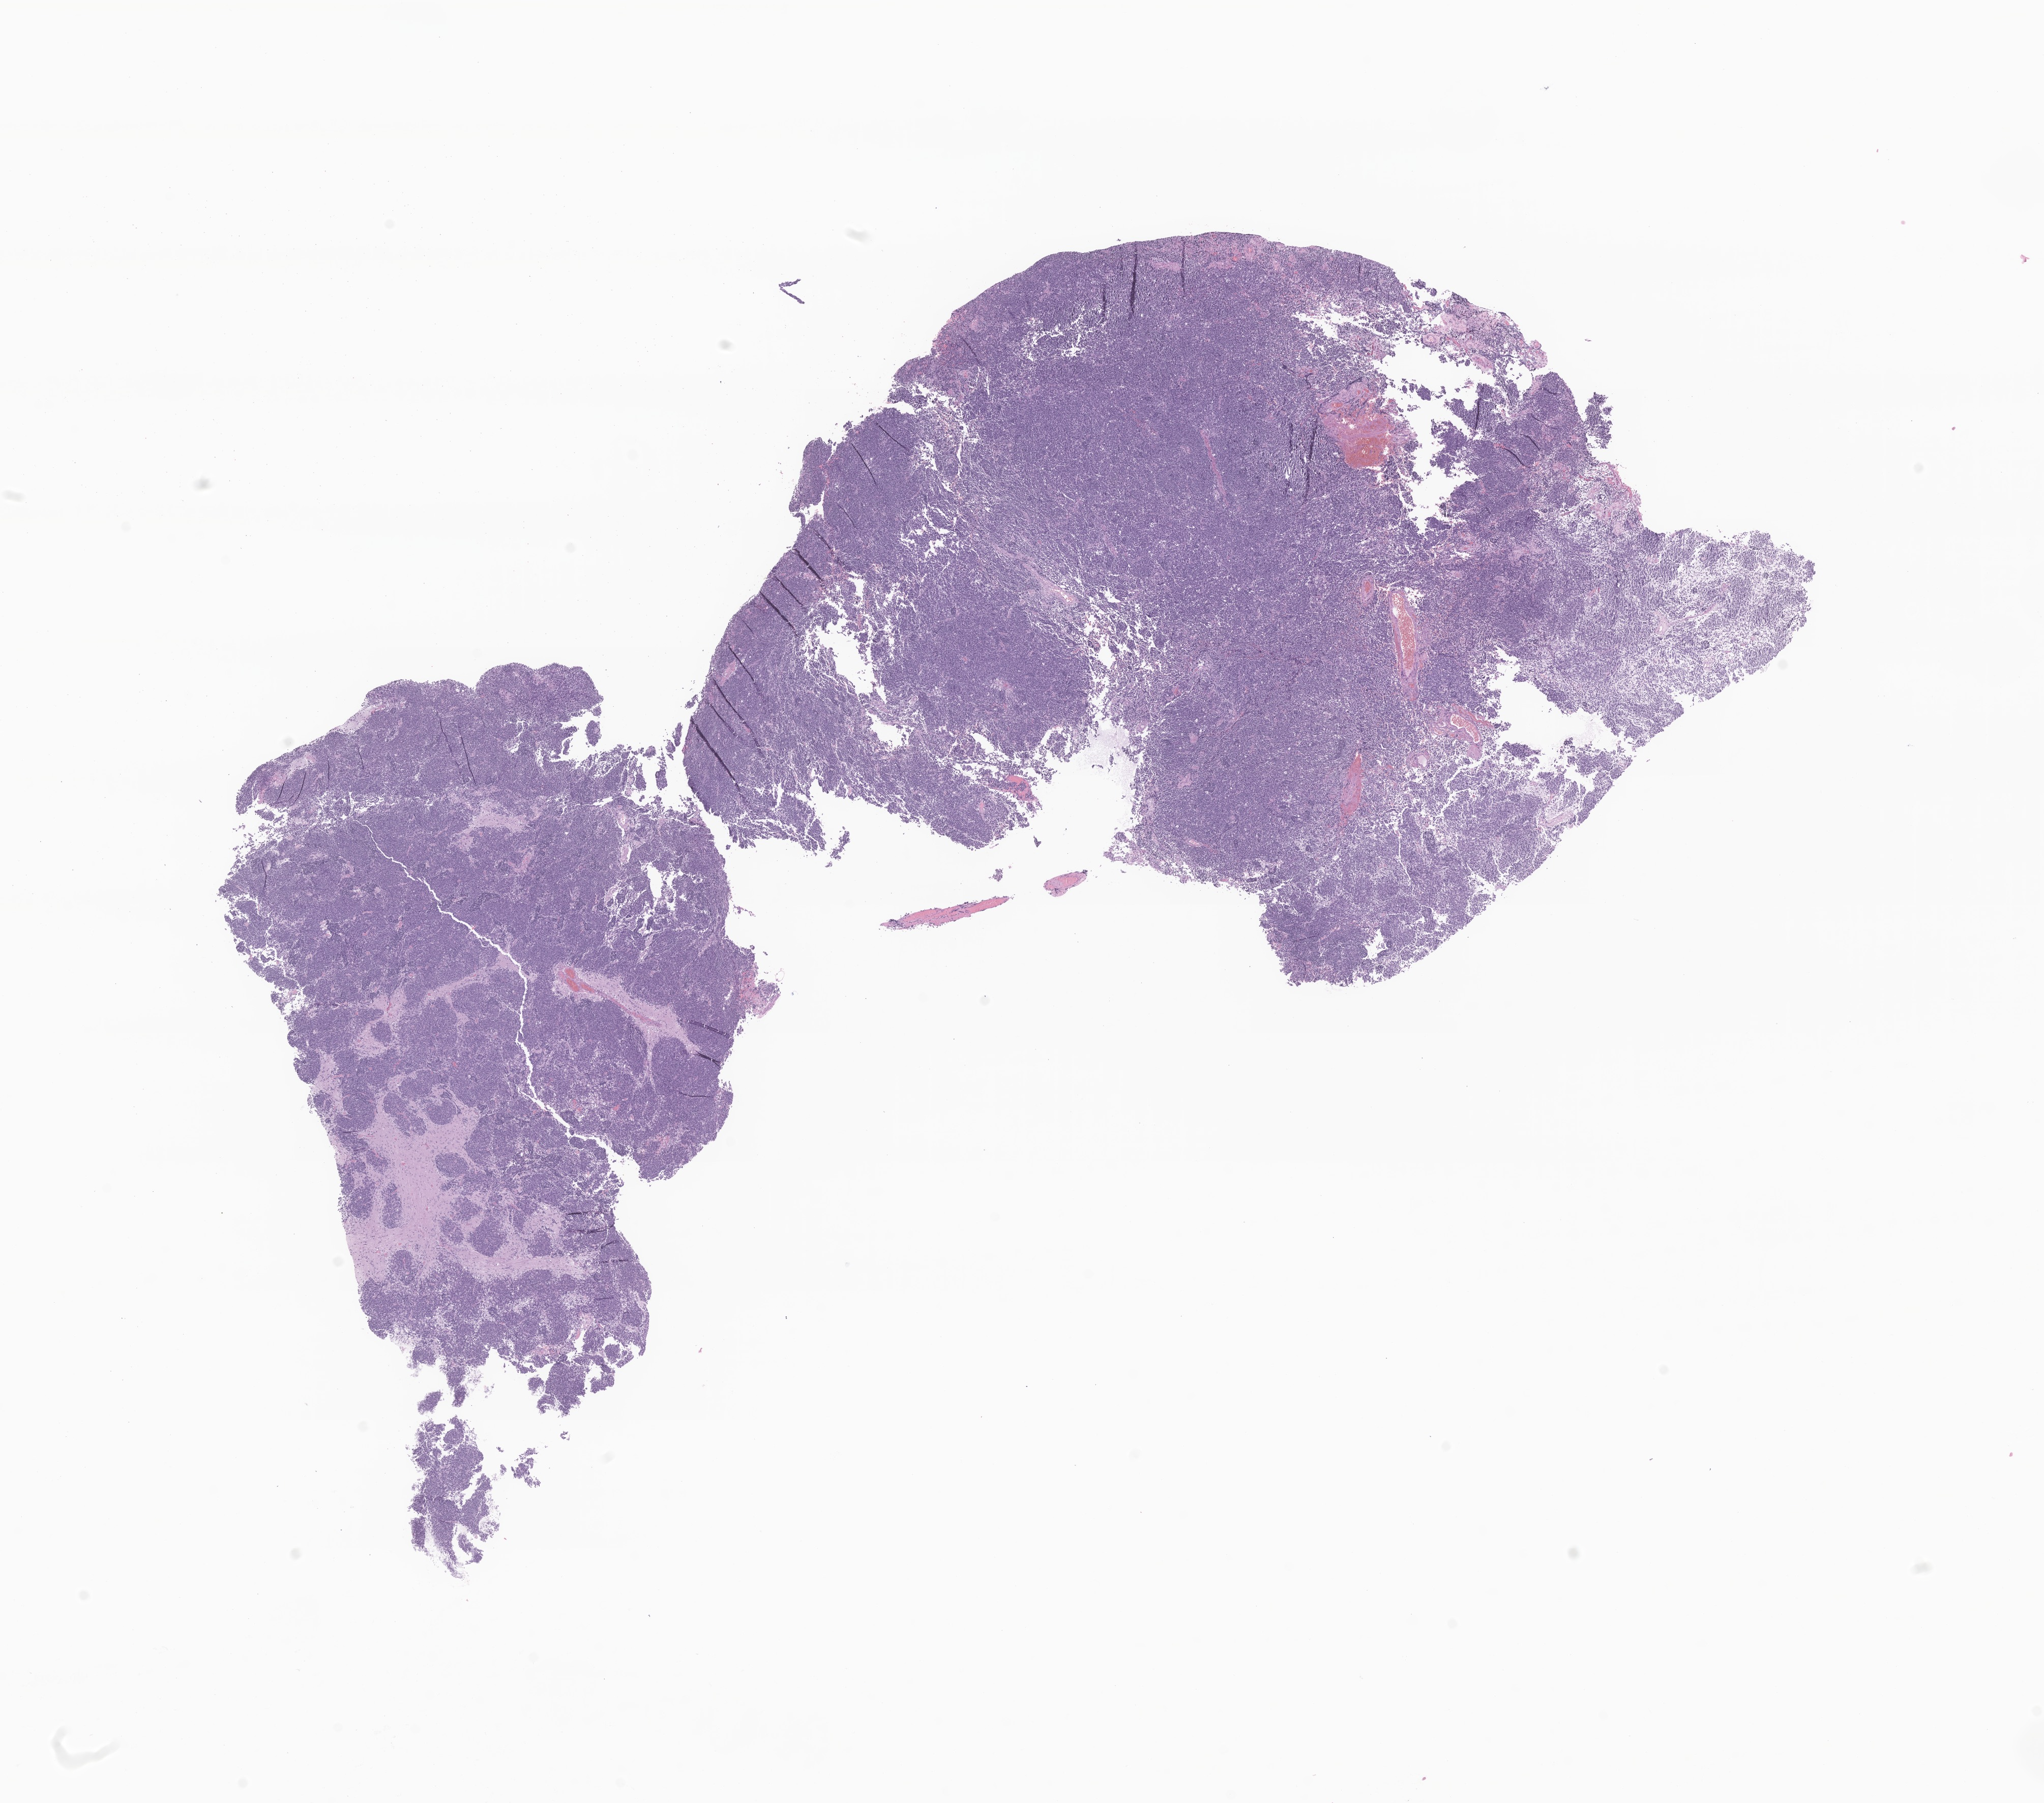
Haematoxylin and eosin whole-slide image of tumor tissue from the brain — shown as a low-resolution overview of the whole scanned area (about 16.9 x 14.9 mm). Formalin-fixed, paraffin-embedded (FFPE) tissue. Patient: female, age 57 months (4 years 9 months).
Diagnosis: Medulloblastoma, NOS.